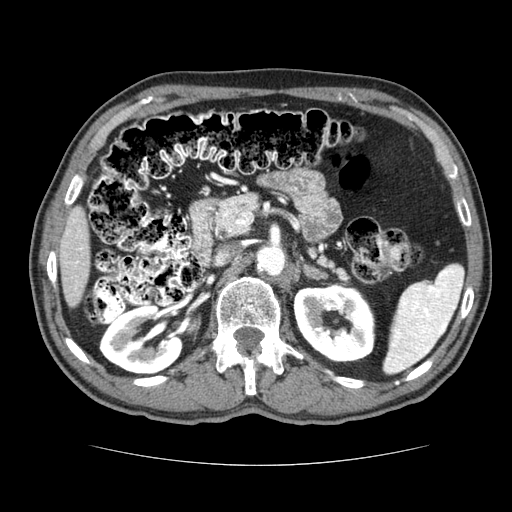
Contrast-enhanced abdominal CT (liver protocol), one axial slice. Reconstruction kernel STANDARD. 120 kVp. Soft-tissue window (W 400 / L 40 HU). 512 × 512 image matrix, field of view 360 × 360 mm. From the clinical record (not read from this slice): diagnosis: hepatocellular carcinoma (patient treated with transarterial chemoembolisation; whether this scan precedes or follows treatment is not stated here); TNM stage (as recorded): Stage-I; Child-Pugh class: A; tumour nodularity: uninodular.
Outlined on this slice (semi-automatic segmentation, software-assisted and operator-edited):
- liver parenchyma outside the tumour (the mass and vessels are separate outlines, so this box may not span the whole liver): bounding box <58,206,90,306> (left, top, right, bottom; pixels)
- liver vessels: <67,219,83,290>